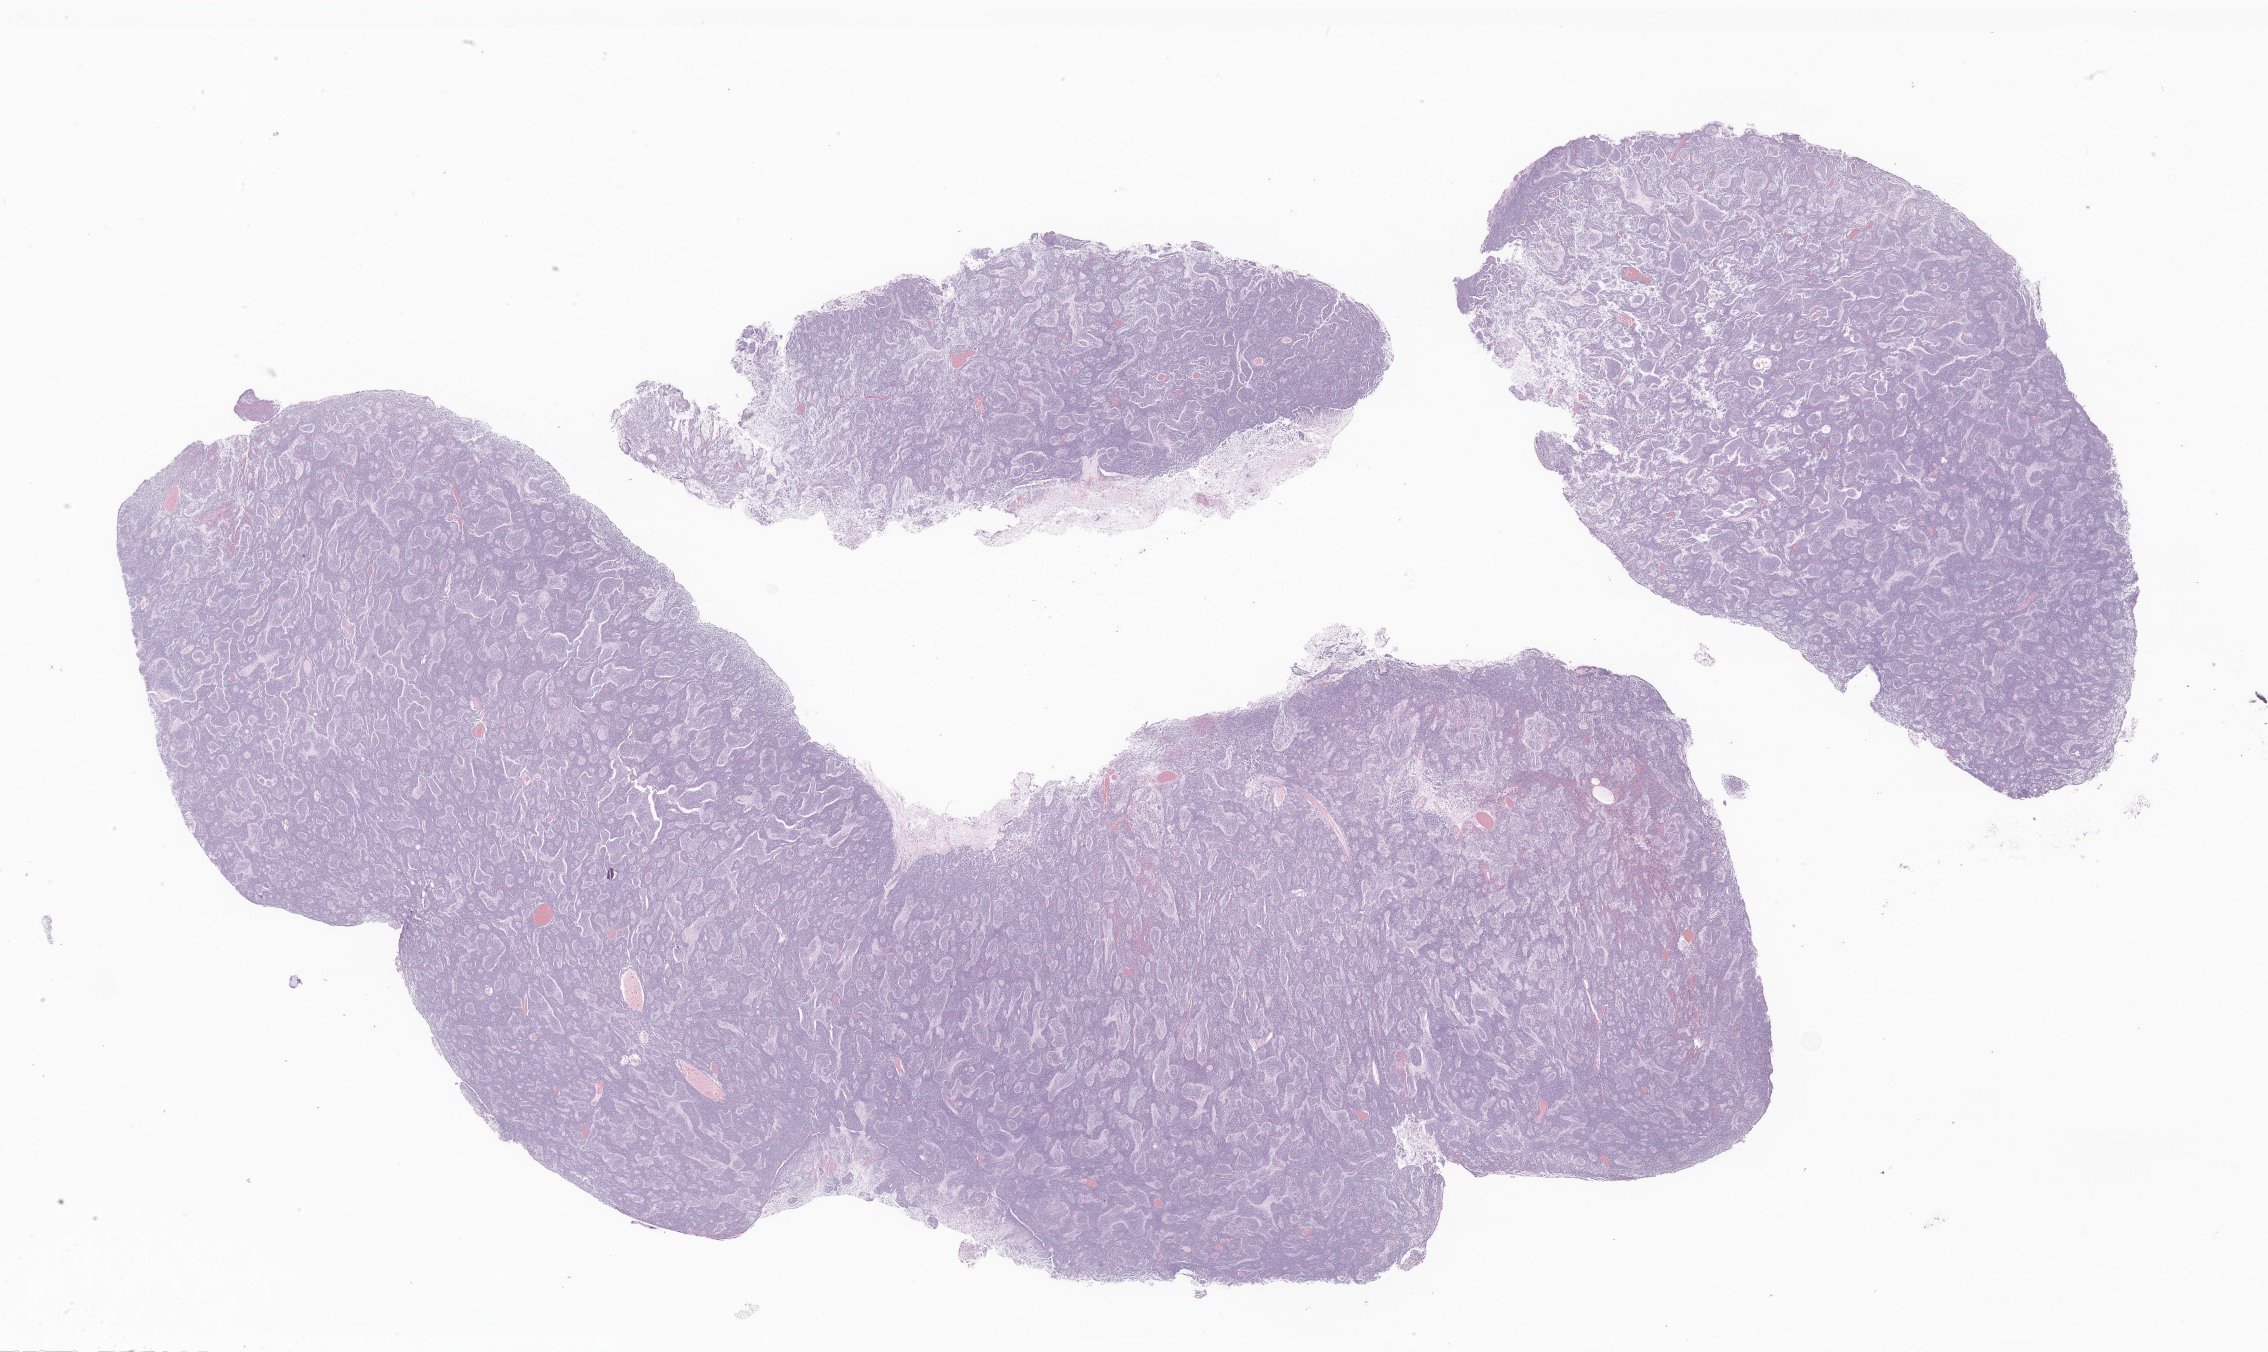
Whole-slide image, H&E stain of tumor tissue from the cerebellum, low-resolution overview of the scanned area, about 38.2 x 22.8 mm; FFPE section. Male patient, age 499 days.
• recorded diagnosis: Medulloblastoma, NOS